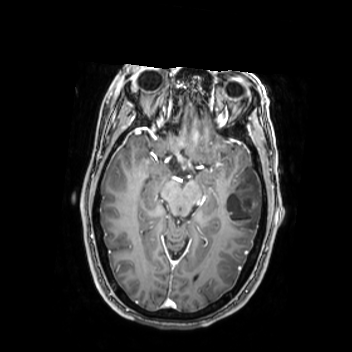
Brain MRI from a brain-tumour surgery series, one axial slice; slice 156 of 350 in the series (ordered by position); T1-weighted post-contrast; 0.9 mm slice thickness; 352 × 352 image matrix, field of view 280 × 280 mm. Case-level facts recorded for this patient, not image findings: histopathology: Oligodendroglioma; WHO grade: 2; IDH mutation: yes; tumour location: Left Middle Temporal Gyrus.
Structures marked on this image (outlined manually by an expert reader):
- tumour: box from (x=224, y=166) to (x=262, y=233) px